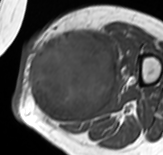
MRI of an extremity soft-tissue mass, one axial slice; position 32 of 65 along the scan axis; MR volume resampled by the dataset authors to the PET/CT grid (not the native acquisition matrix); 3.27 mm slice thickness; 163 × 155 image matrix, field of view 159 × 151 mm. Female patient. Case-level facts recorded for this patient, not image findings: histological type: pleomorphic leiomyosarcoma; grade: high; site of the primary tumour: left thigh.
Annotated regions visible in this slice (expert contour drawn on MRI and transferred to this co-registered scan by the dataset authors):
- gross tumour volume including surrounding oedema: box from (x=26, y=28) to (x=118, y=125) px
- gross tumour volume (mass): (x=26, y=31)–(x=116, y=123)